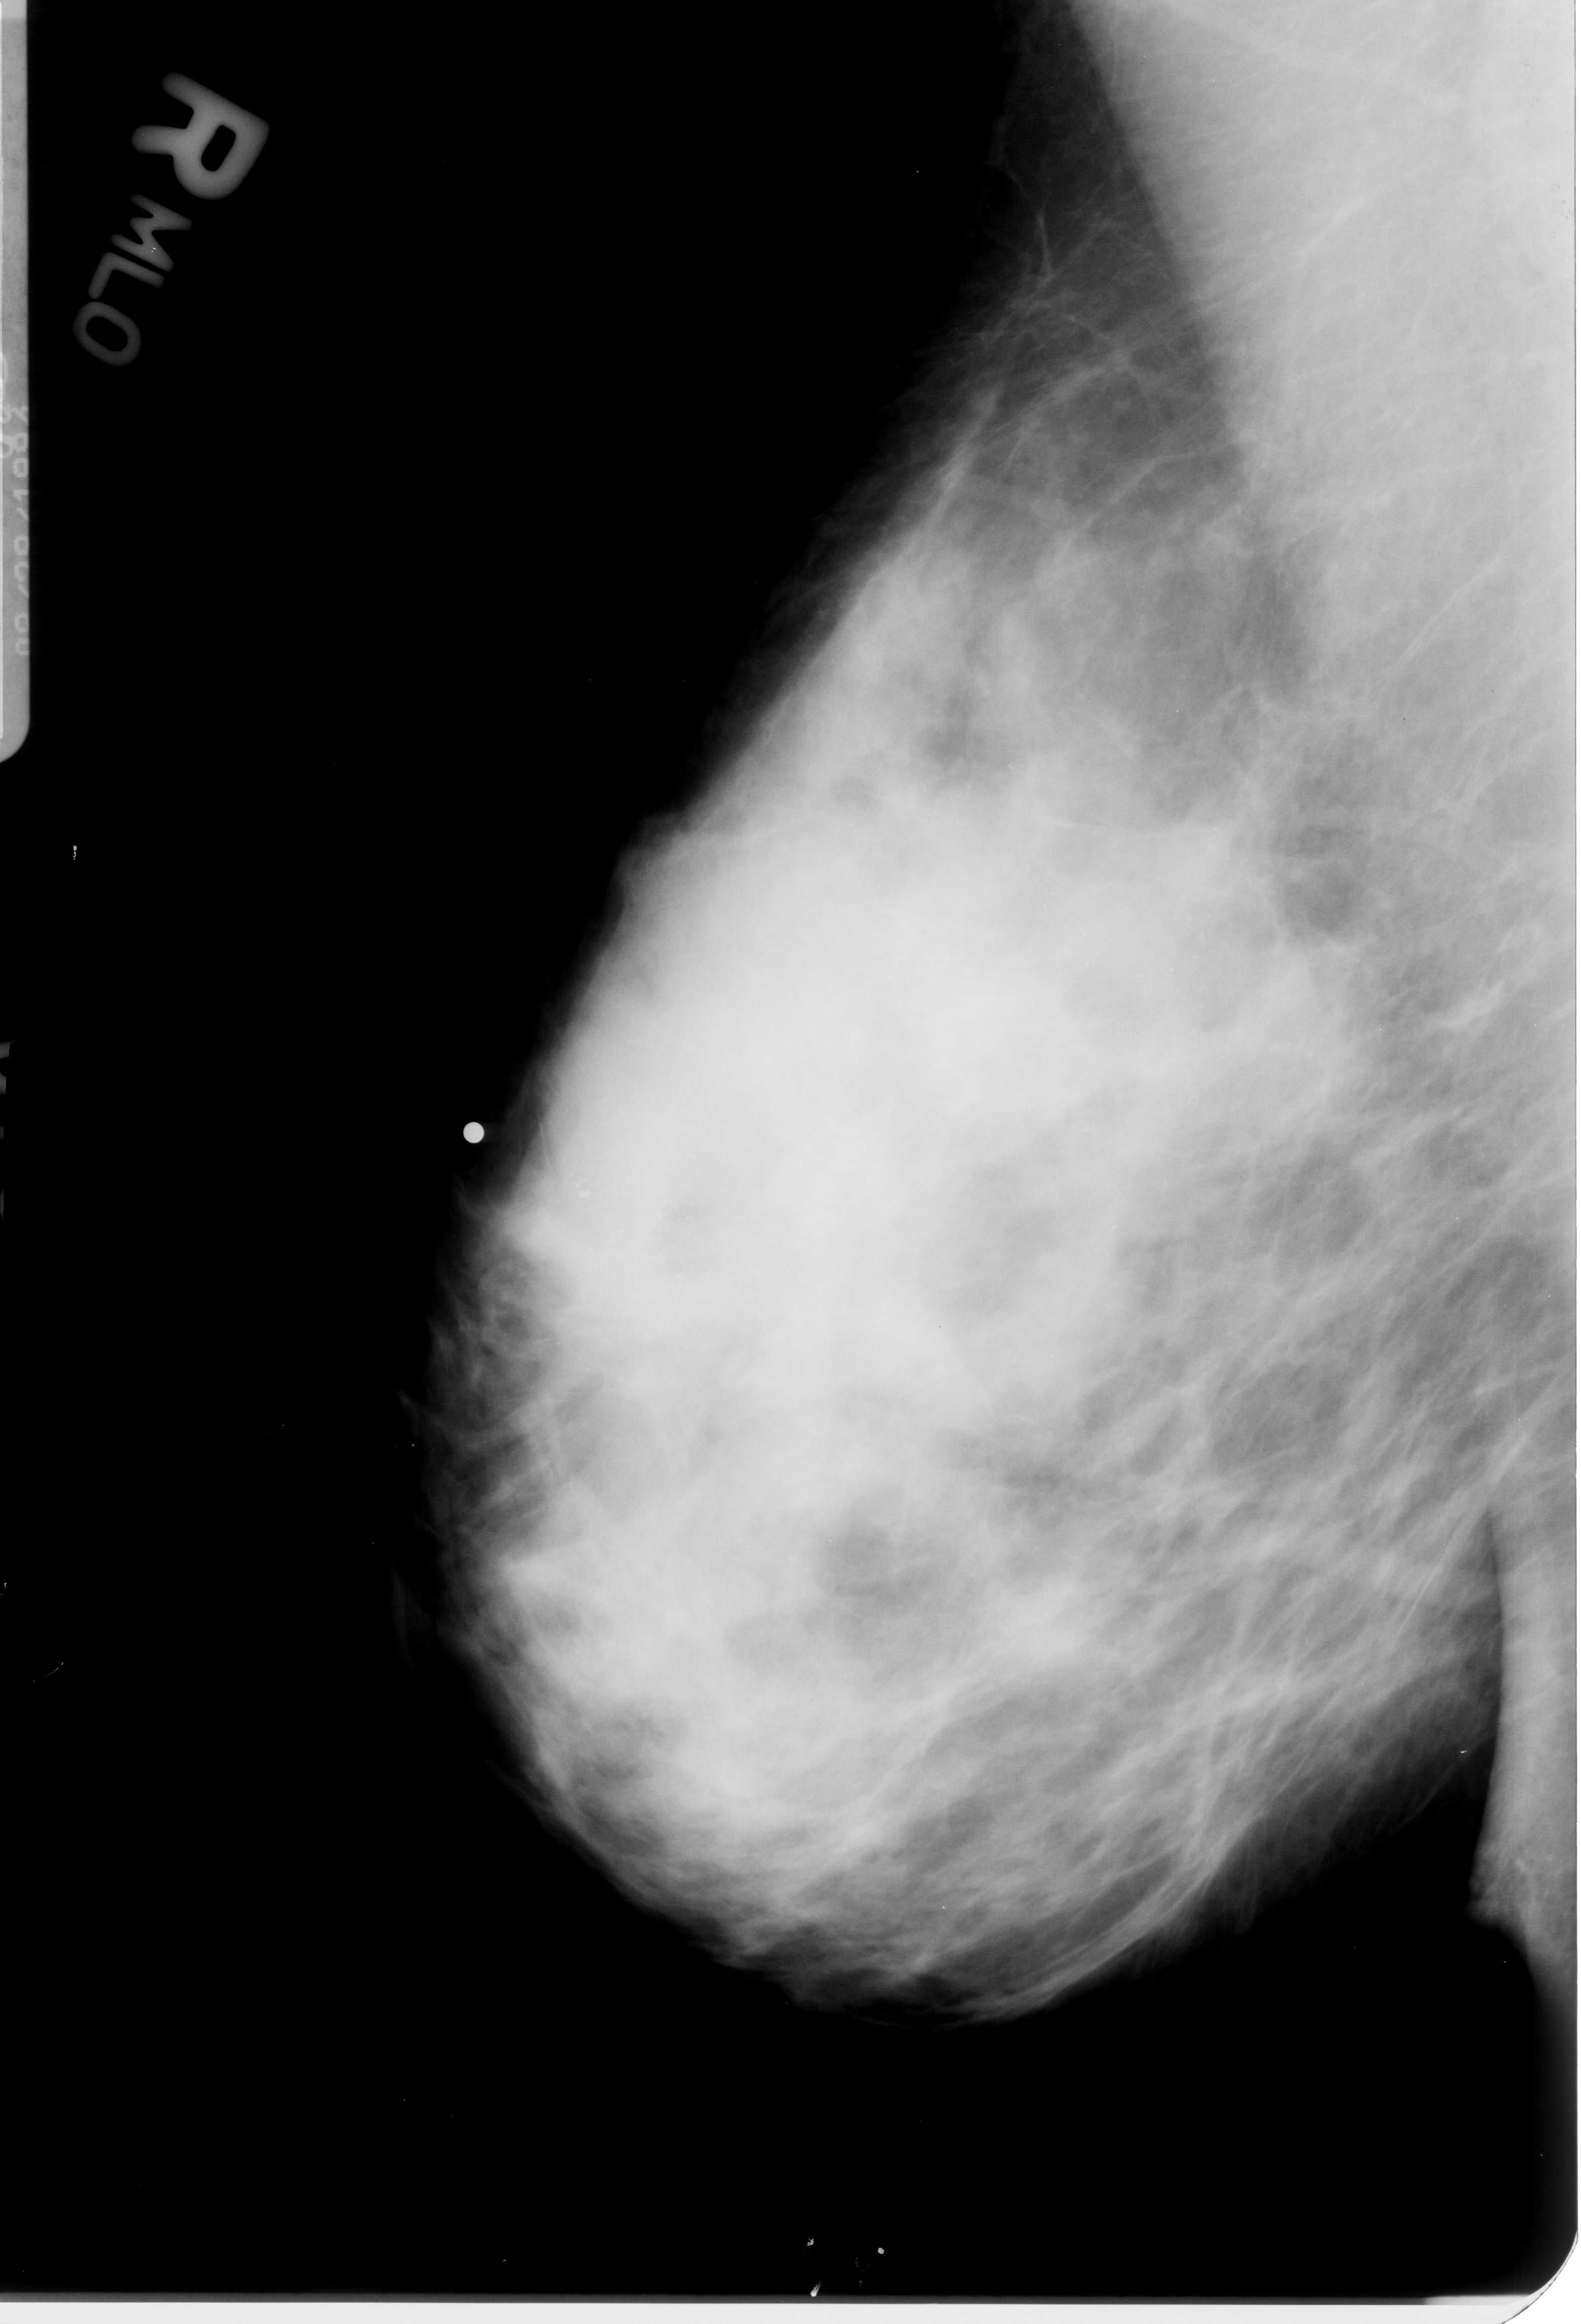
Mammogram (digitized film), right breast, mediolateral oblique (MLO) view.
Calcifications, morphology pleomorphic, distribution regional; BI-RADS assessment category 5; subtlety rating 3 on a 1 (subtle) to 5 (obvious) scale; pathology result (as recorded, not read from the image): malignant.